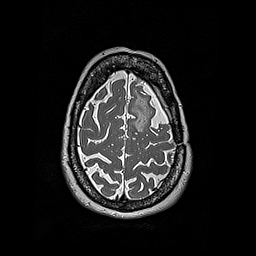
Brain MRI from a brain-tumour surgery series, one axial slice; slice 146 of 192 in the series (ordered by position); 1 mm slice thickness; 256 × 256 image matrix, field of view 250 × 250 mm. From the clinical record (not read from this slice): histopathology: Oligodendroglioma; WHO grade: 2; IDH mutation: yes; tumour location: Left Frontal.
Annotated regions visible in this slice (outlined manually by an expert reader):
- tumour: bounding box <147,112,152,122> (left, top, right, bottom; pixels)